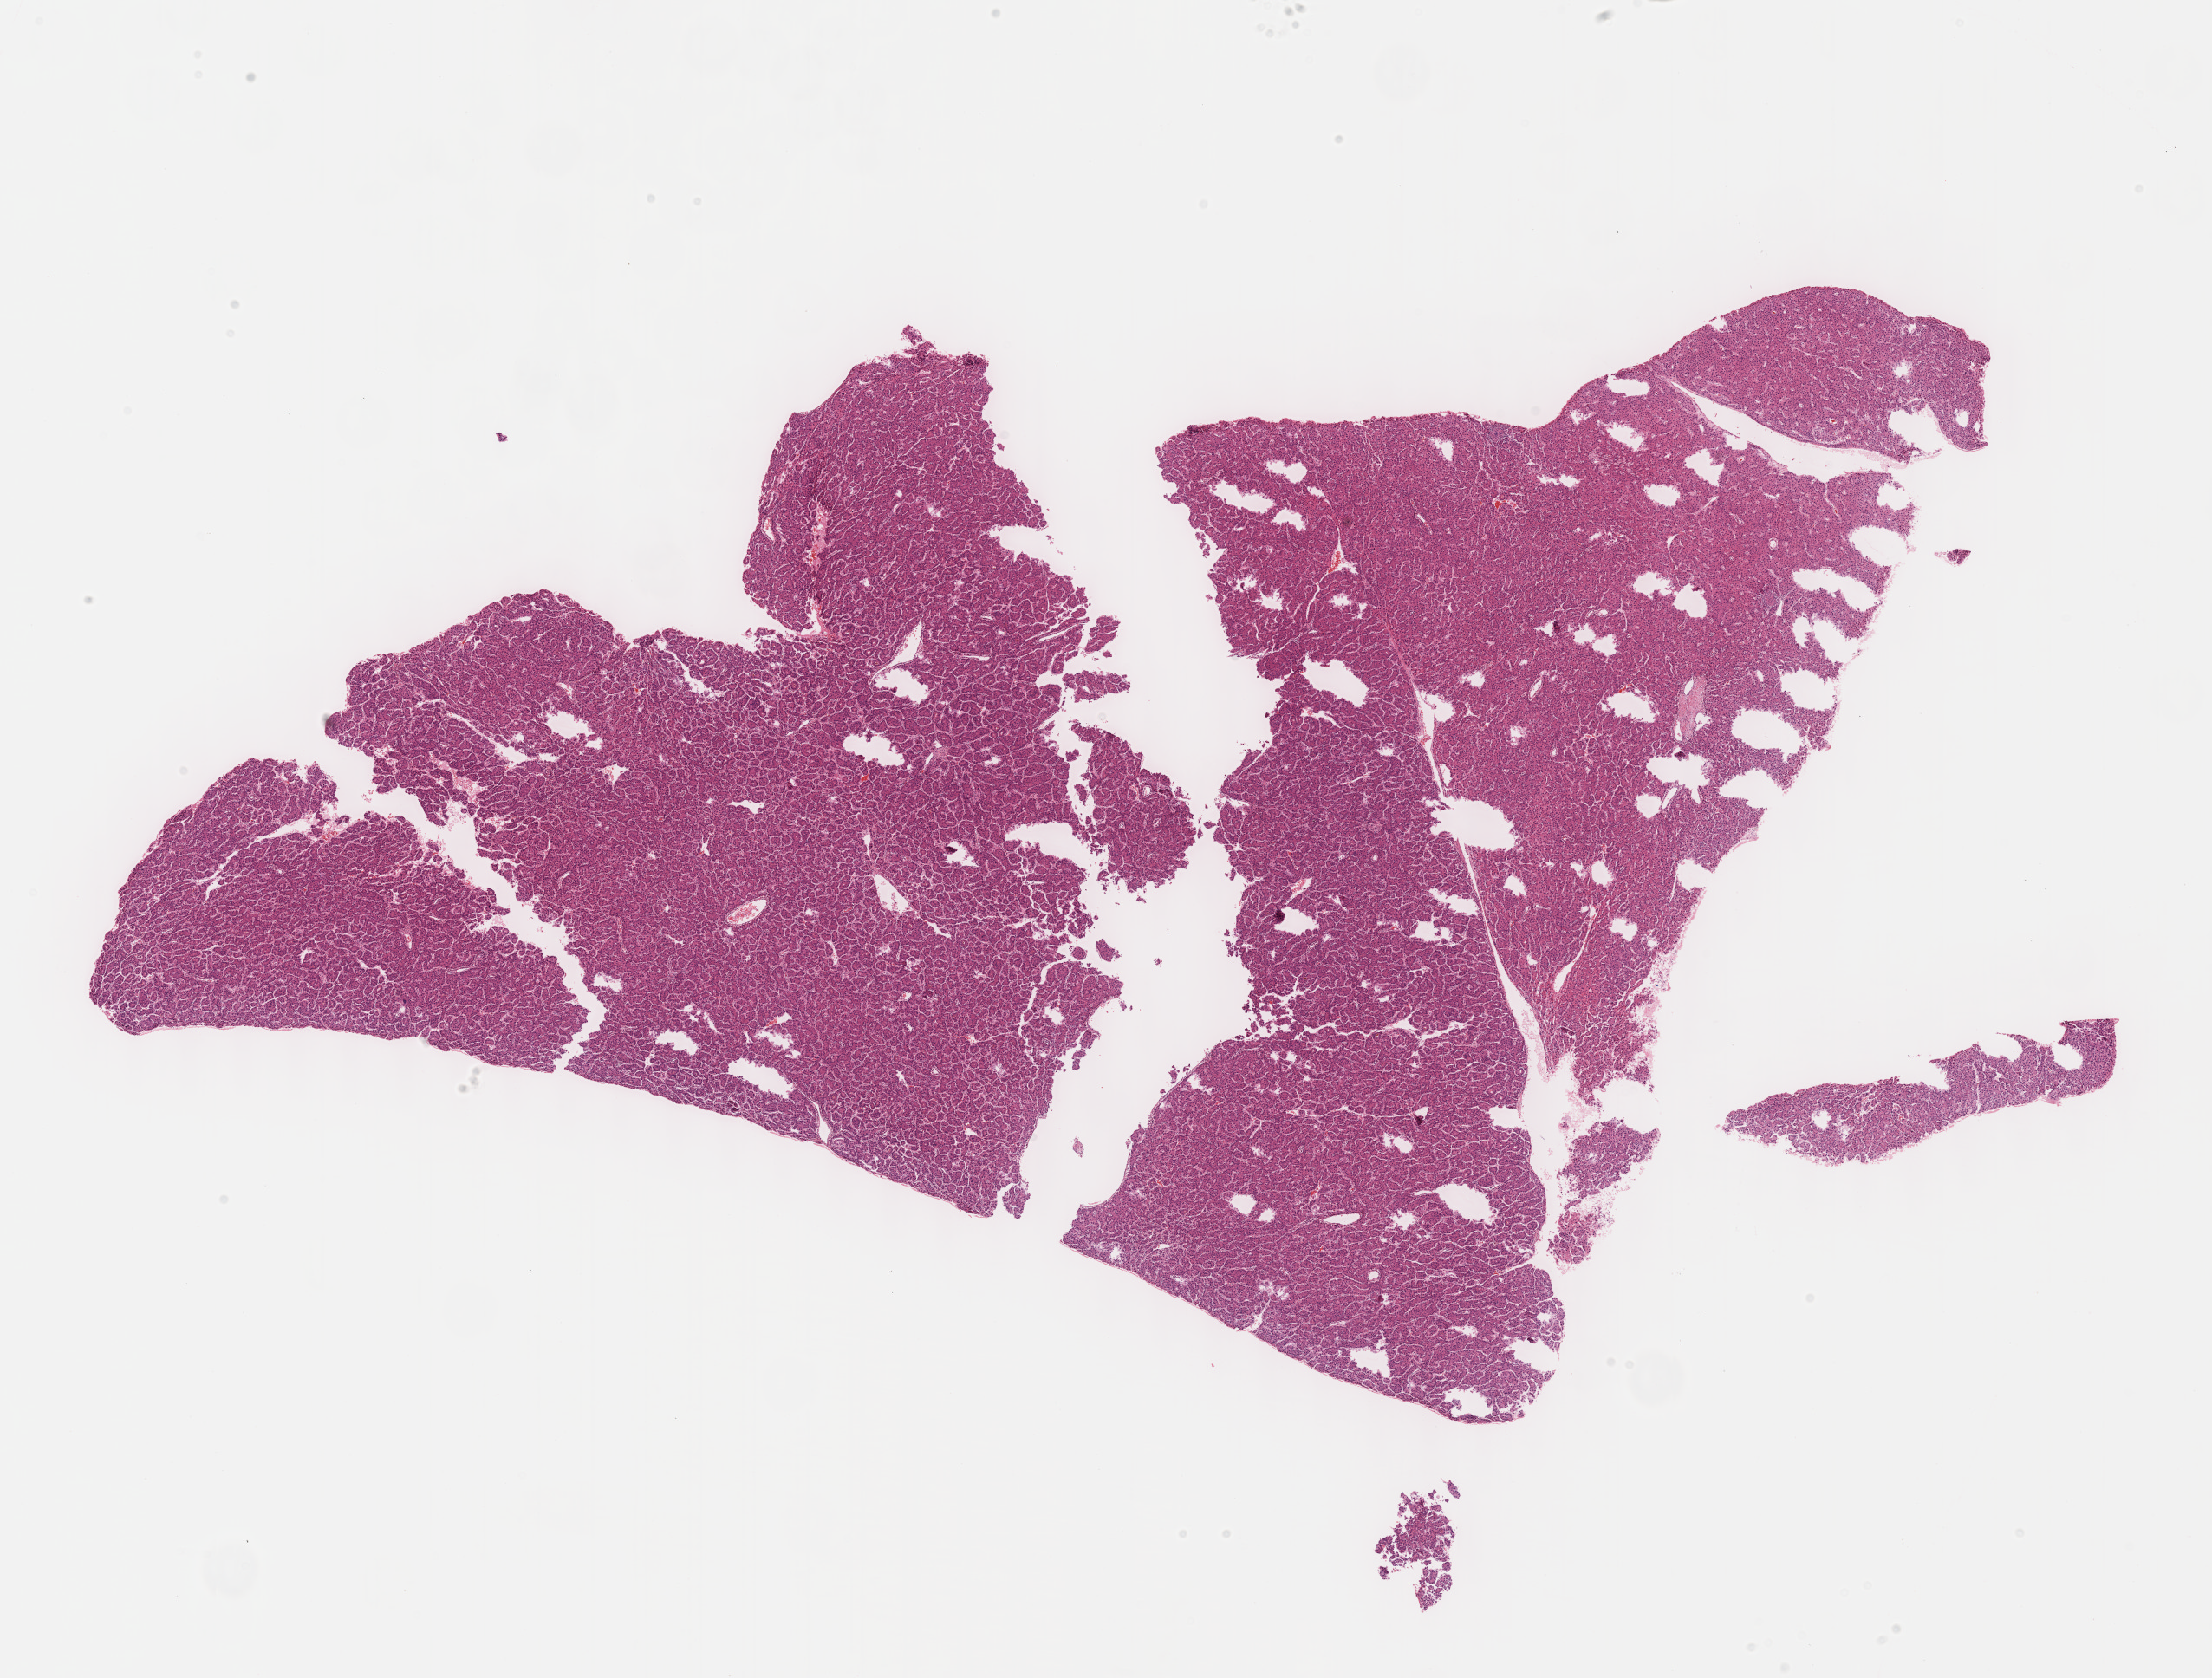
Digitized H&E tissue section (whole slide), whole scanned area (about 20.6 x 15.6 mm, acquisition: 40x scan) shown as a low-resolution overview, formalin-fixed paraffin-embedded (FFPE) diagnostic section, liver, primary tumour sample. Male patient; age at initial diagnosis 50 years. Histologic grade: G4 (undifferentiated).
TNM: T1 N0 M0. AJCC pathologic stage: I. Diagnosis: Hepatocellular carcinoma, NOS.